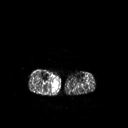
FDG PET of an extremity soft-tissue mass (from a PET/CT study), one axial slice. Slice 123 of 267 in the series (ordered by position). 3.27 mm slice thickness. 128 × 128 image matrix, field of view 500 × 500 mm. Patient: male, 69 years. Case-level facts recorded for this patient, not image findings: histological type: pleiomorphic liposarcoma; grade: high; site of the primary tumour: right calf.
Outlined on this slice (expert contour drawn on MRI and transferred to this co-registered scan by the dataset authors):
- gross tumour volume including surrounding oedema: bounding box <51,79,58,89> (left, top, right, bottom; pixels)